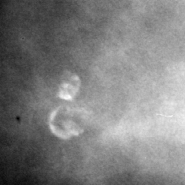
Region of interest cut from a scanned film mammogram (one marked finding); right breast; CC view; BI-RADS breast density category 3 (scale 1–4).
- Marked abnormality: calcifications, morphology lucent center; BI-RADS assessment category 2; benign; no additional work-up was recommended (benign without callback).